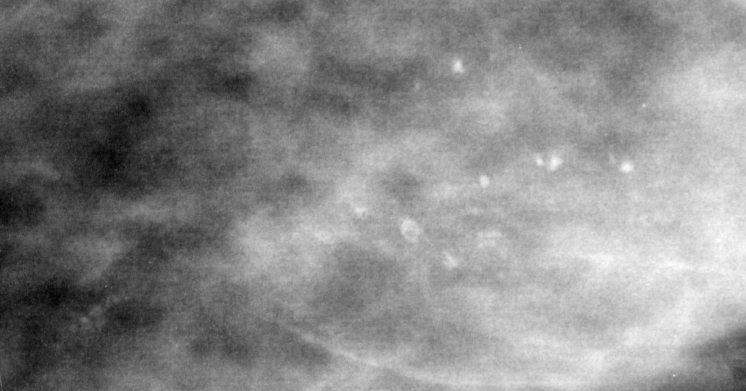
Crop from a digitized film mammogram around one marked abnormality; left breast; CC view.
- Calcifications, morphology pleomorphic, distribution linear; BI-RADS assessment category 4; subtlety rating 3 on a 1 (subtle) to 5 (obvious) scale; pathology (as recorded): malignant.